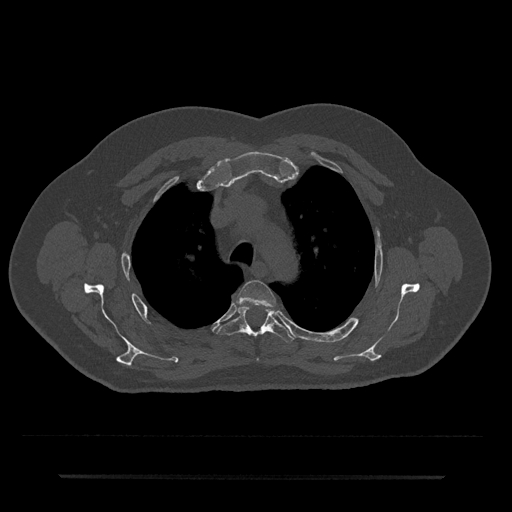
CT including the spine, one axial slice; reconstruction kernel Br40s/3; 120 kVp; bone window (W 1800 / L 400 HU); 0.5 mm slice thickness; 512 × 512 image matrix, field of view 437 × 437 mm. Male patient, age 69 years. From the clinical record (not read from this slice): primary cancer: prostate.
Structures marked on this image (semi-automatically segmented with operator editing):
- T3 vertebra: box from (x=237, y=280) to (x=276, y=307) px
- T4 vertebra: (x=217, y=305)–(x=294, y=342)